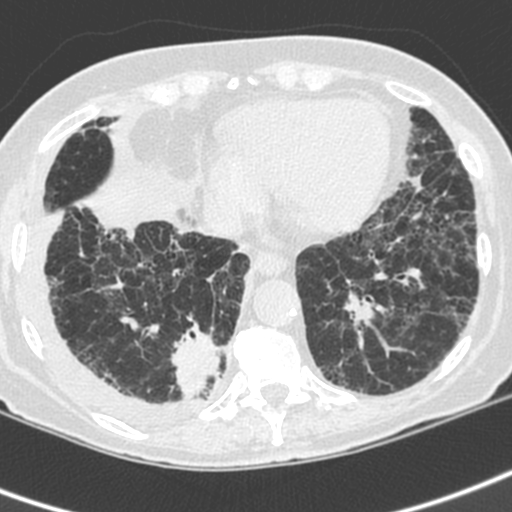
Chest CT (low-dose screening protocol), one axial image; baseline screening round; lung window (W 1500 / L -600 HU); 1.3 mm slice thickness; 512 × 512 image matrix. Female, age 73 years at enrolment. Current smoker at enrolment.
• Lesion marked by an expert reader, box from (x=156, y=317) to (x=235, y=406) px.
• The exam's reader record, not a measurement of the box and not confirmed to be the same lesion: non-calcified nodule or mass ≥4 mm, right lower lobe, 35 × 30 mm, spiculated (stellate) margins, soft tissue attenuation.
• Participant outcome: lung cancer diagnosed 22 days after this screen — adenocarcinoma, NOS, right lower lobe, stage IV (AJCC 6th edition), 35 mm at pathology.